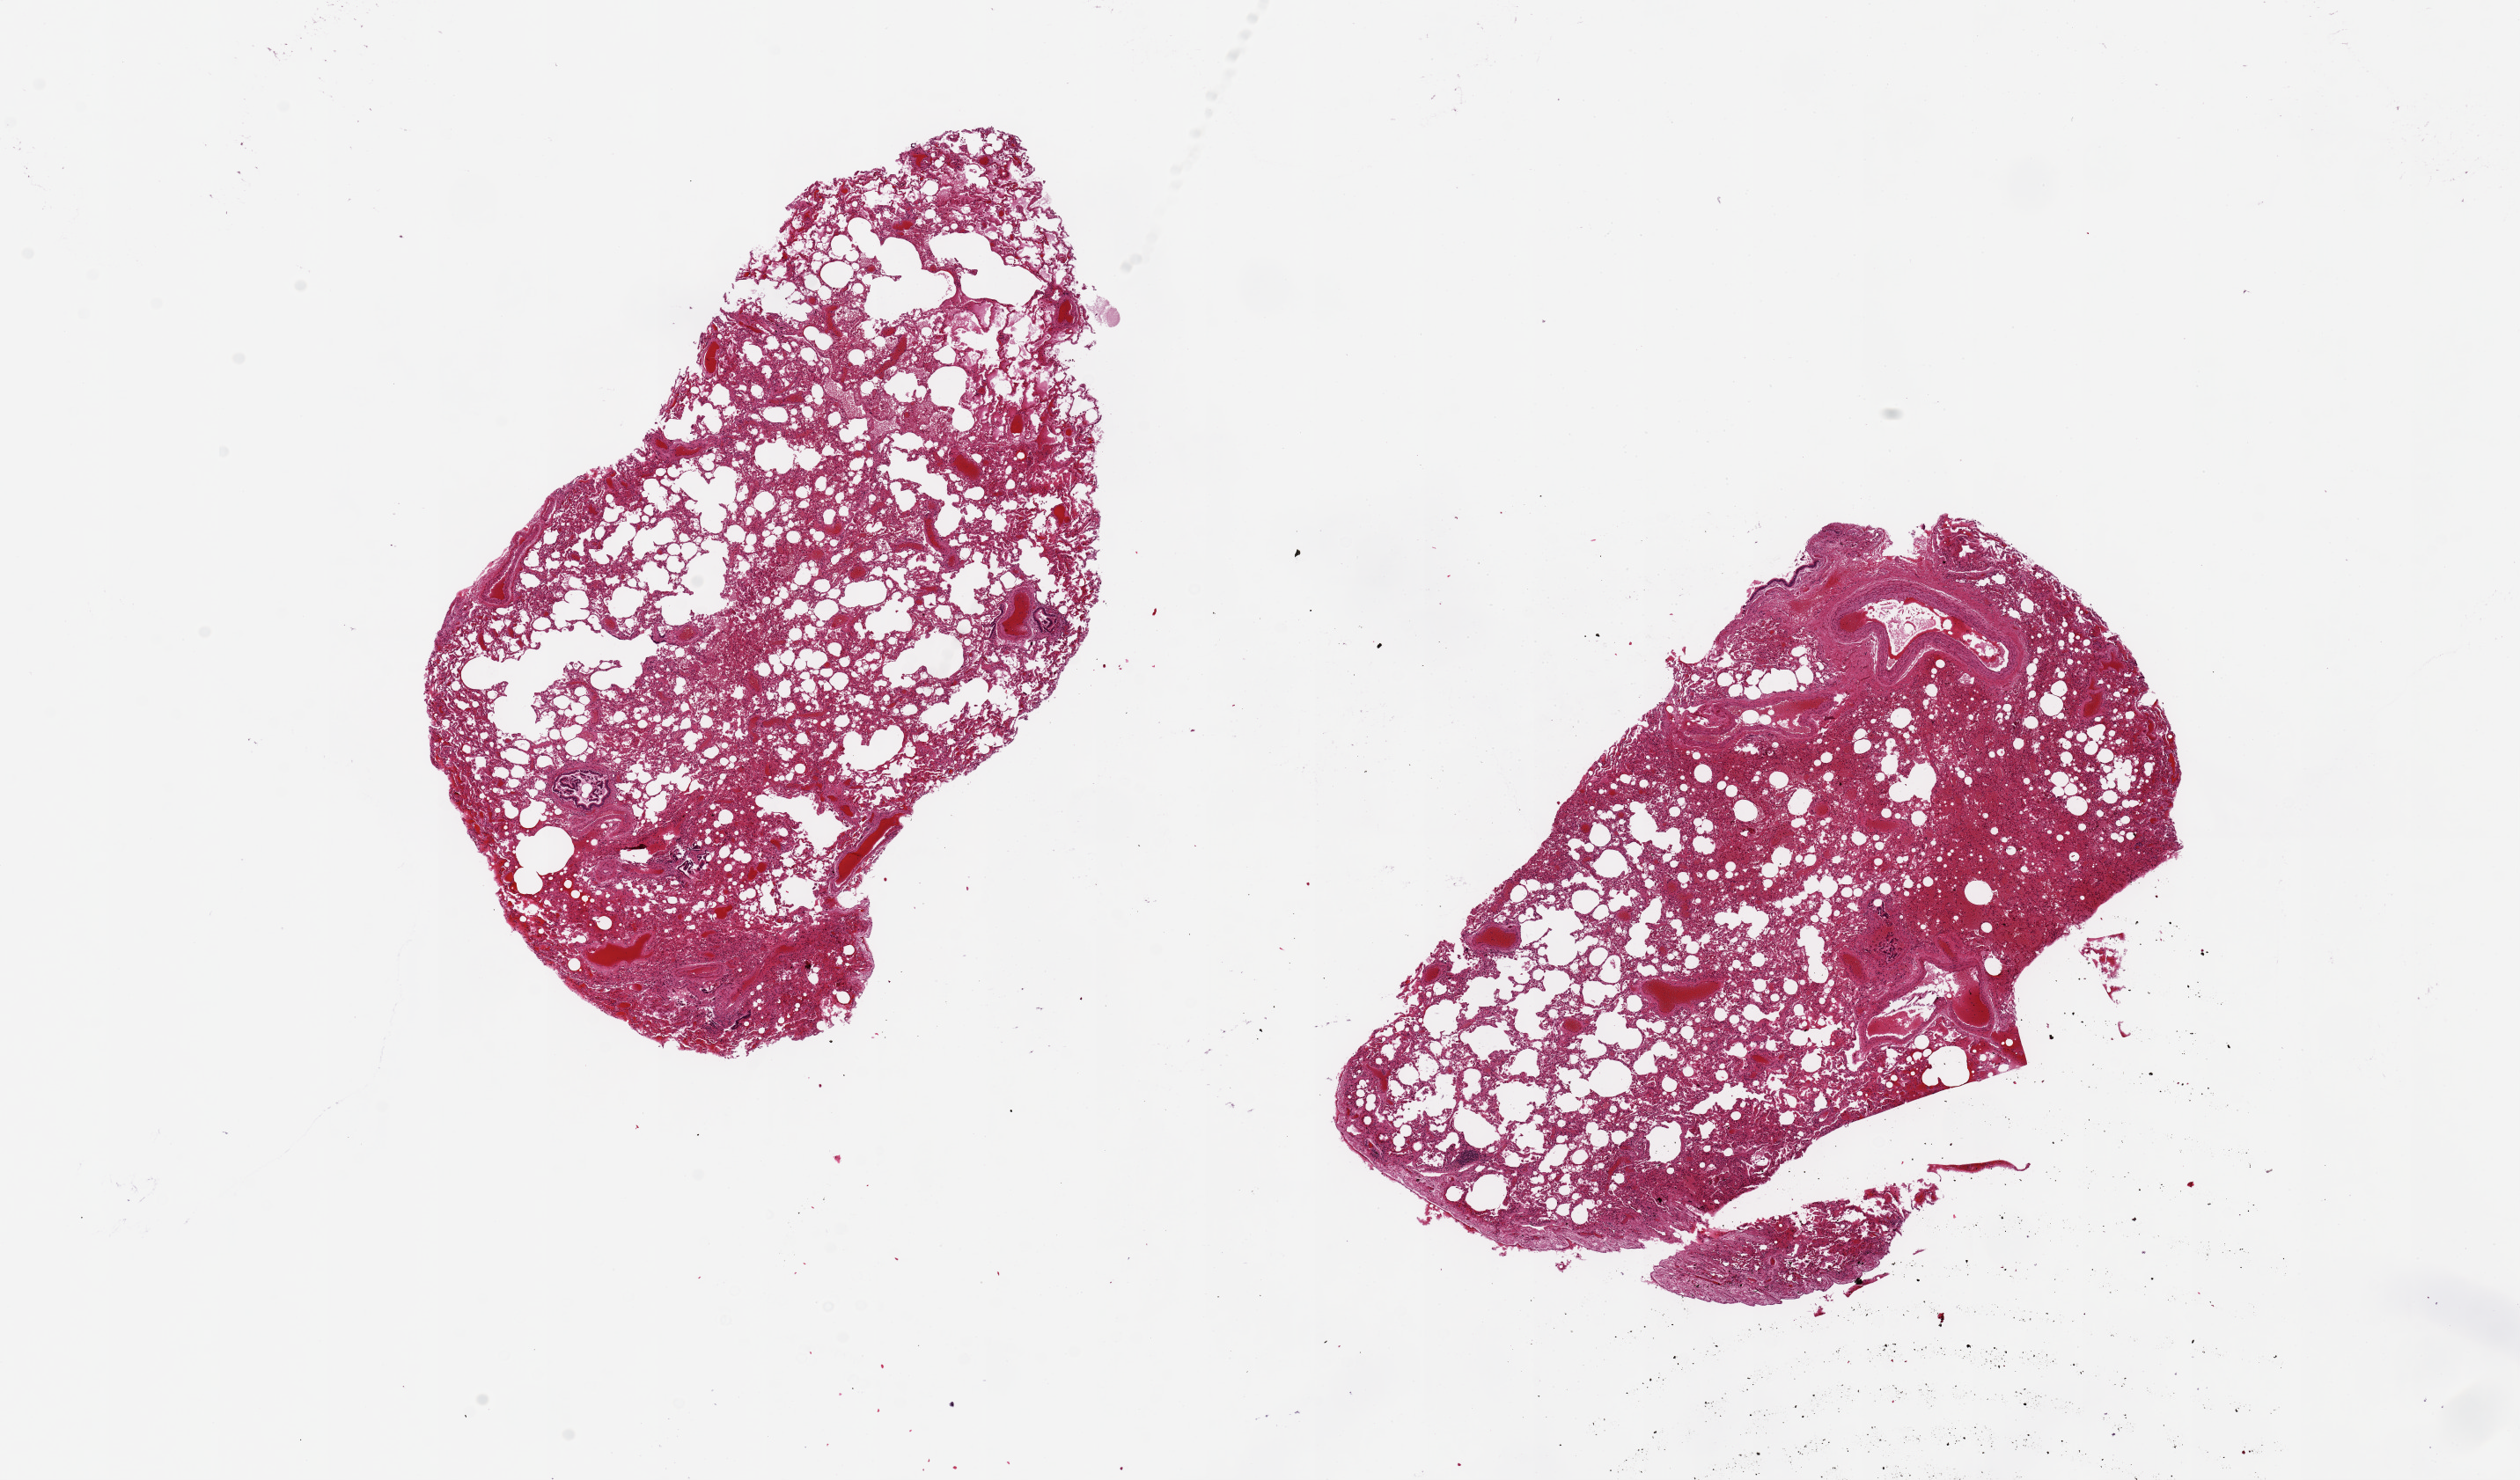
Haematoxylin and eosin whole-slide image, shown as a low-resolution overview of the whole scanned area (about 22.6 x 13.3 mm, slide scanned at 20x). PAXgene-fixed, paraffin-embedded tissue. Sampled site (target tissue): lung. Tissue donor sample. Donor sex: male.
Pathologist's review note for this sample: 2 pieces ~7x4mm. Apparent emphysematous changes but extremly autolyzed.